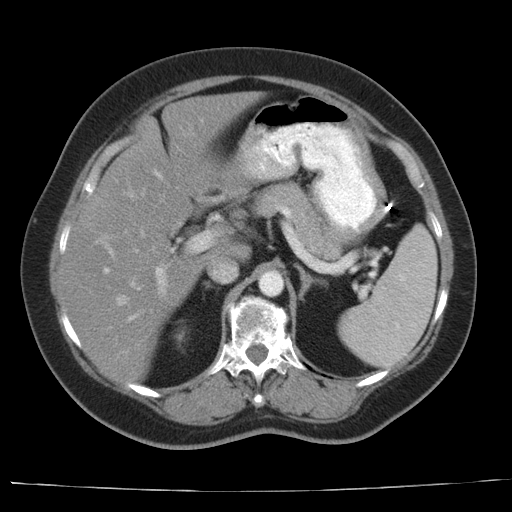
Contrast-enhanced abdominal CT, one axial slice; position 20 of 44 along the scan axis; intravenous contrast given; soft-tissue window (W 400 / L 40 HU); 5 mm slice thickness; 512 × 512 image matrix, field of view 373 × 373 mm. Female patient. Case-level facts recorded for this patient, not image findings: diagnosis: colorectal cancer liver metastases, imaged before liver resection; multiple liver metastases: yes; largest metastasis: 1.8 cm.
Outlined on this slice (expert manual segmentation):
- hepatic veins: bounding box [x1, y1, x2, y2] px = [117, 191, 133, 305]
- liver: [58, 92, 262, 384]
- planned liver remnant (the part of the liver to remain after resection): [106, 92, 261, 263]
- portal vein (with intrahepatic branches): [95, 119, 213, 321]